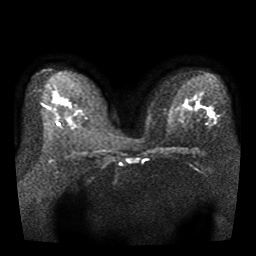
Breast MRI, one axial slice. Position 22 of 41 along the scan axis. Diffusion-weighted series; image 2 of 4 stored at this slice position (different b-values; order by instance number). 1.5 T. 5 mm slice thickness. 256 × 256 image matrix, field of view 330 × 330 mm. Female patient.
Annotated regions visible in this slice (expert manual segmentation):
- tumour on diffusion-weighted imaging: box from (x=208, y=111) to (x=212, y=117) px